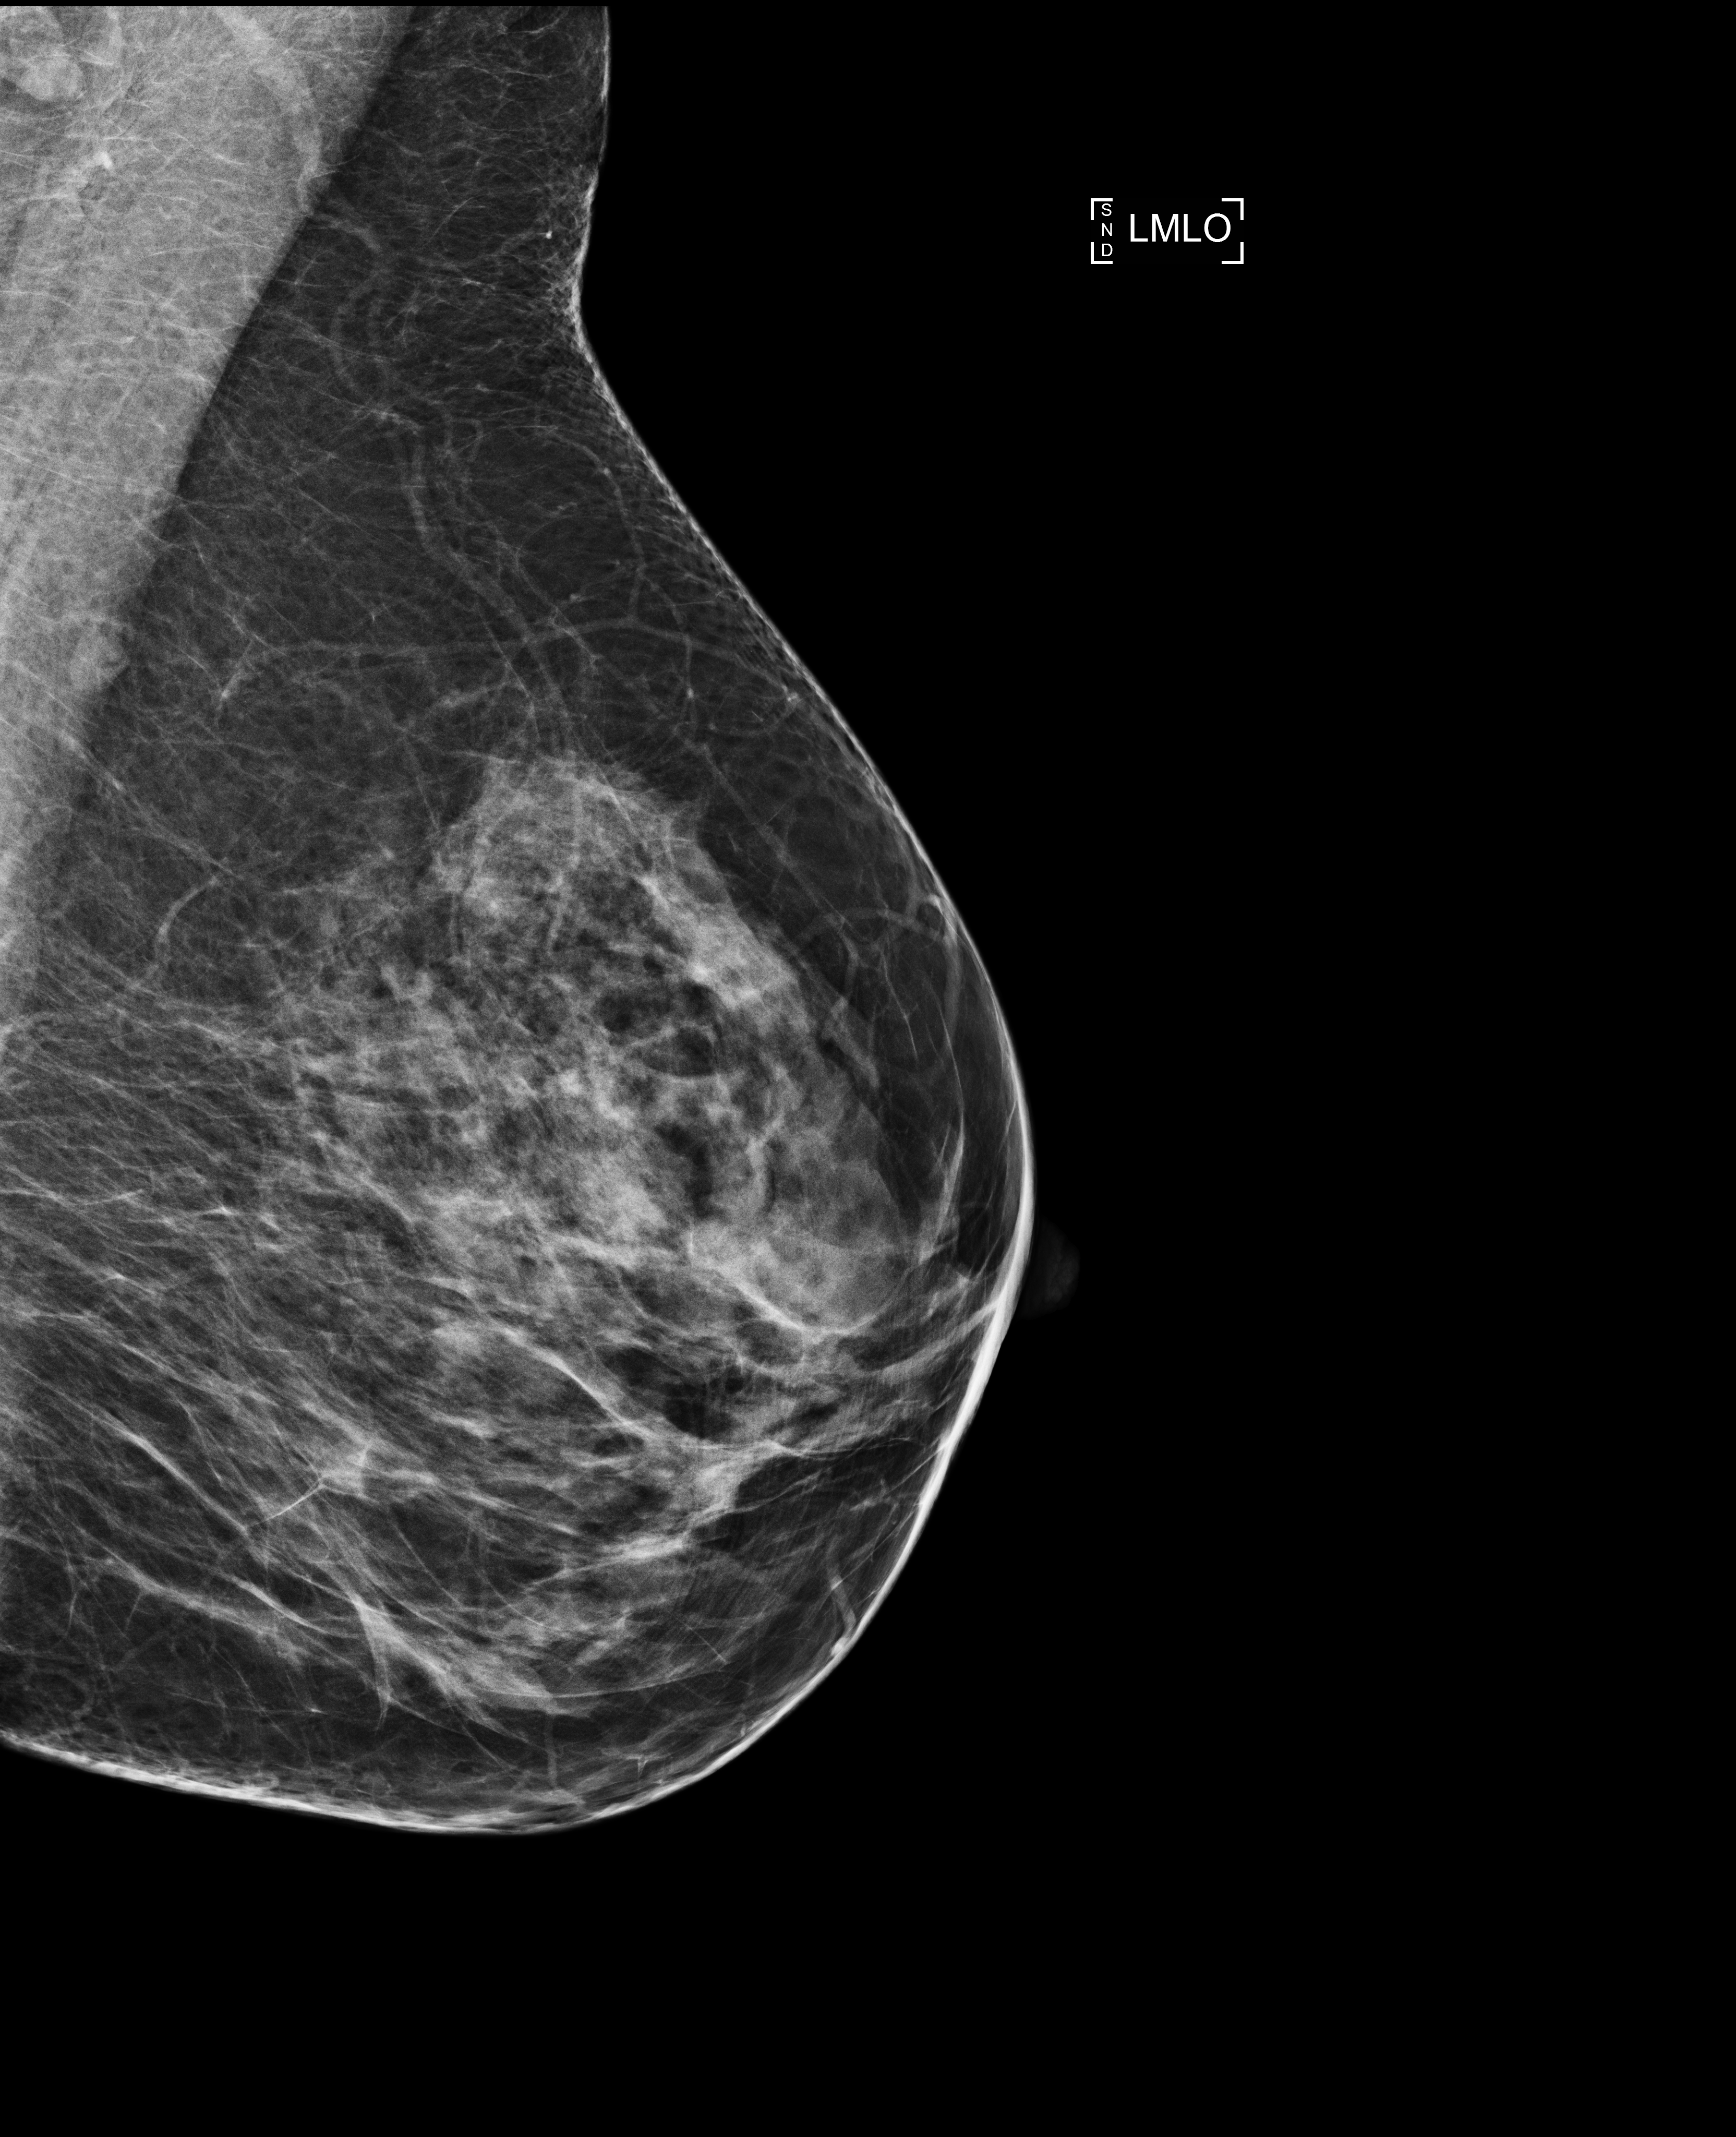
Screening examination; compressed breast thickness 54 mm. Female patient, age 54 years.
Image type: full-field digital mammogram. Breast: left. Projection: MLO view.